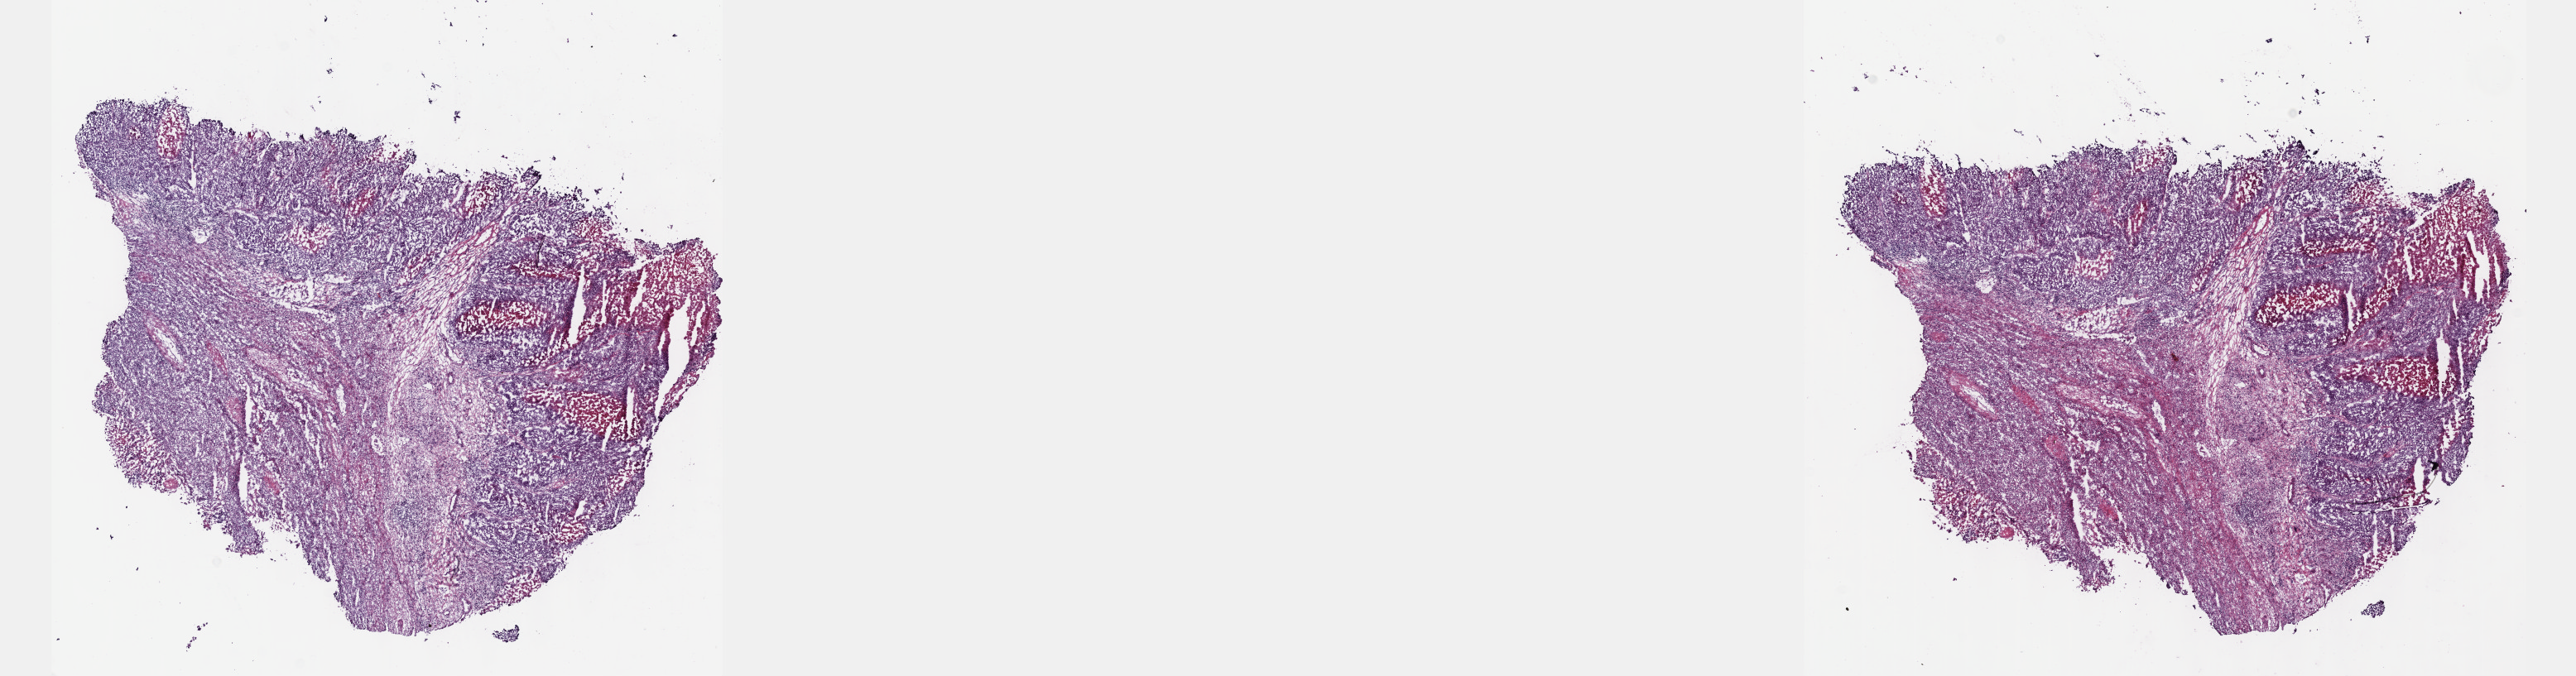
Whole-slide histology image, Hematoxylin and eosin (H&E) stained, whole scanned area (about 25.1 x 6.6 mm, from a 40x scan) shown as a low-resolution overview; frozen section from the top of the tissue portion; additional metastatic tumour sample. Male patient; age at initial diagnosis 55 years. Composition of this section per pathologist review: tumour cells 70%, tumour nuclei 70%, normal cells 0%, stromal cells 24%, necrosis 6%. Infiltration values recorded for this section: lymphocyte infiltration 4%, monocyte infiltration 1%, neutrophil infiltration 1%.
- this section: metastatic tumour tissue
- patient diagnosis: Malignant melanoma, NOS